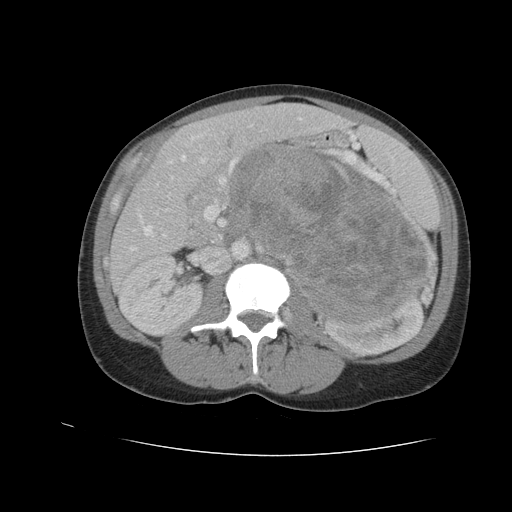
Contrast-enhanced abdominal CT, one axial slice; slice 57 of 90 in the series (ordered by position); reconstruction kernel STANDARD; 120 kVp; soft-tissue window (W 400 / L 40 HU); 5 mm slice thickness; 512 × 512 image matrix. Female patient. Case-level facts recorded for this patient, not image findings: diagnosis: adrenocortical carcinoma; tumour side: left adrenal; tumour size at pathology: 18 cm; Ki-67 index: 11 %.
Annotated regions visible in this slice (semi-automatic segmentation, software-assisted and operator-edited):
- mass: bounding box (x1, y1, x2, y2) in pixels: (234, 148, 427, 322)